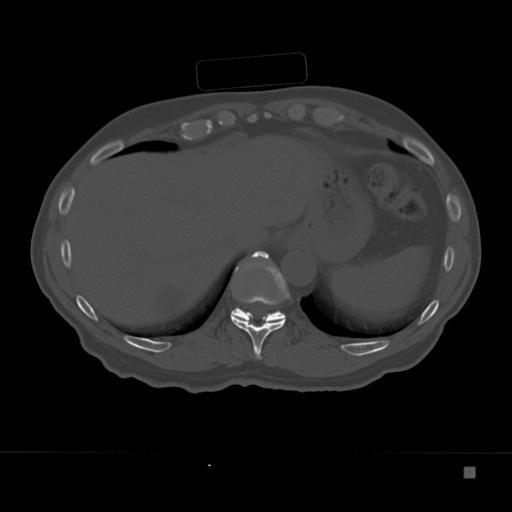
CT including the spine, one axial slice. Position 165 of 332 along the scan axis. 120 kVp. Bone window (W 1800 / L 400 HU). 1.5 mm slice thickness. 512 × 512 image matrix, field of view 389 × 389 mm. Male patient, age 72 years. From the clinical record (not read from this slice): primary cancer: skeletal.
Structures marked on this image (semi-automatically segmented with operator editing):
- T10 vertebra: bounding box (x1, y1, x2, y2) in pixels: (230, 251, 290, 359)
- T11 vertebra: (232, 251, 285, 323)